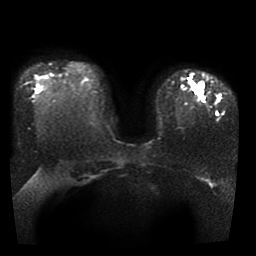
Breast MRI, one axial slice; position 28 of 41 along the scan axis; diffusion-weighted series; image 2 of 4 stored at this slice position (different b-values; order by instance number); 1.5 T; 5 mm slice thickness; 256 × 256 image matrix, field of view 330 × 330 mm. Female patient.
Outlined on this slice (manually delineated by an expert):
- tumour on diffusion-weighted imaging: box from (x=187, y=78) to (x=203, y=100) px